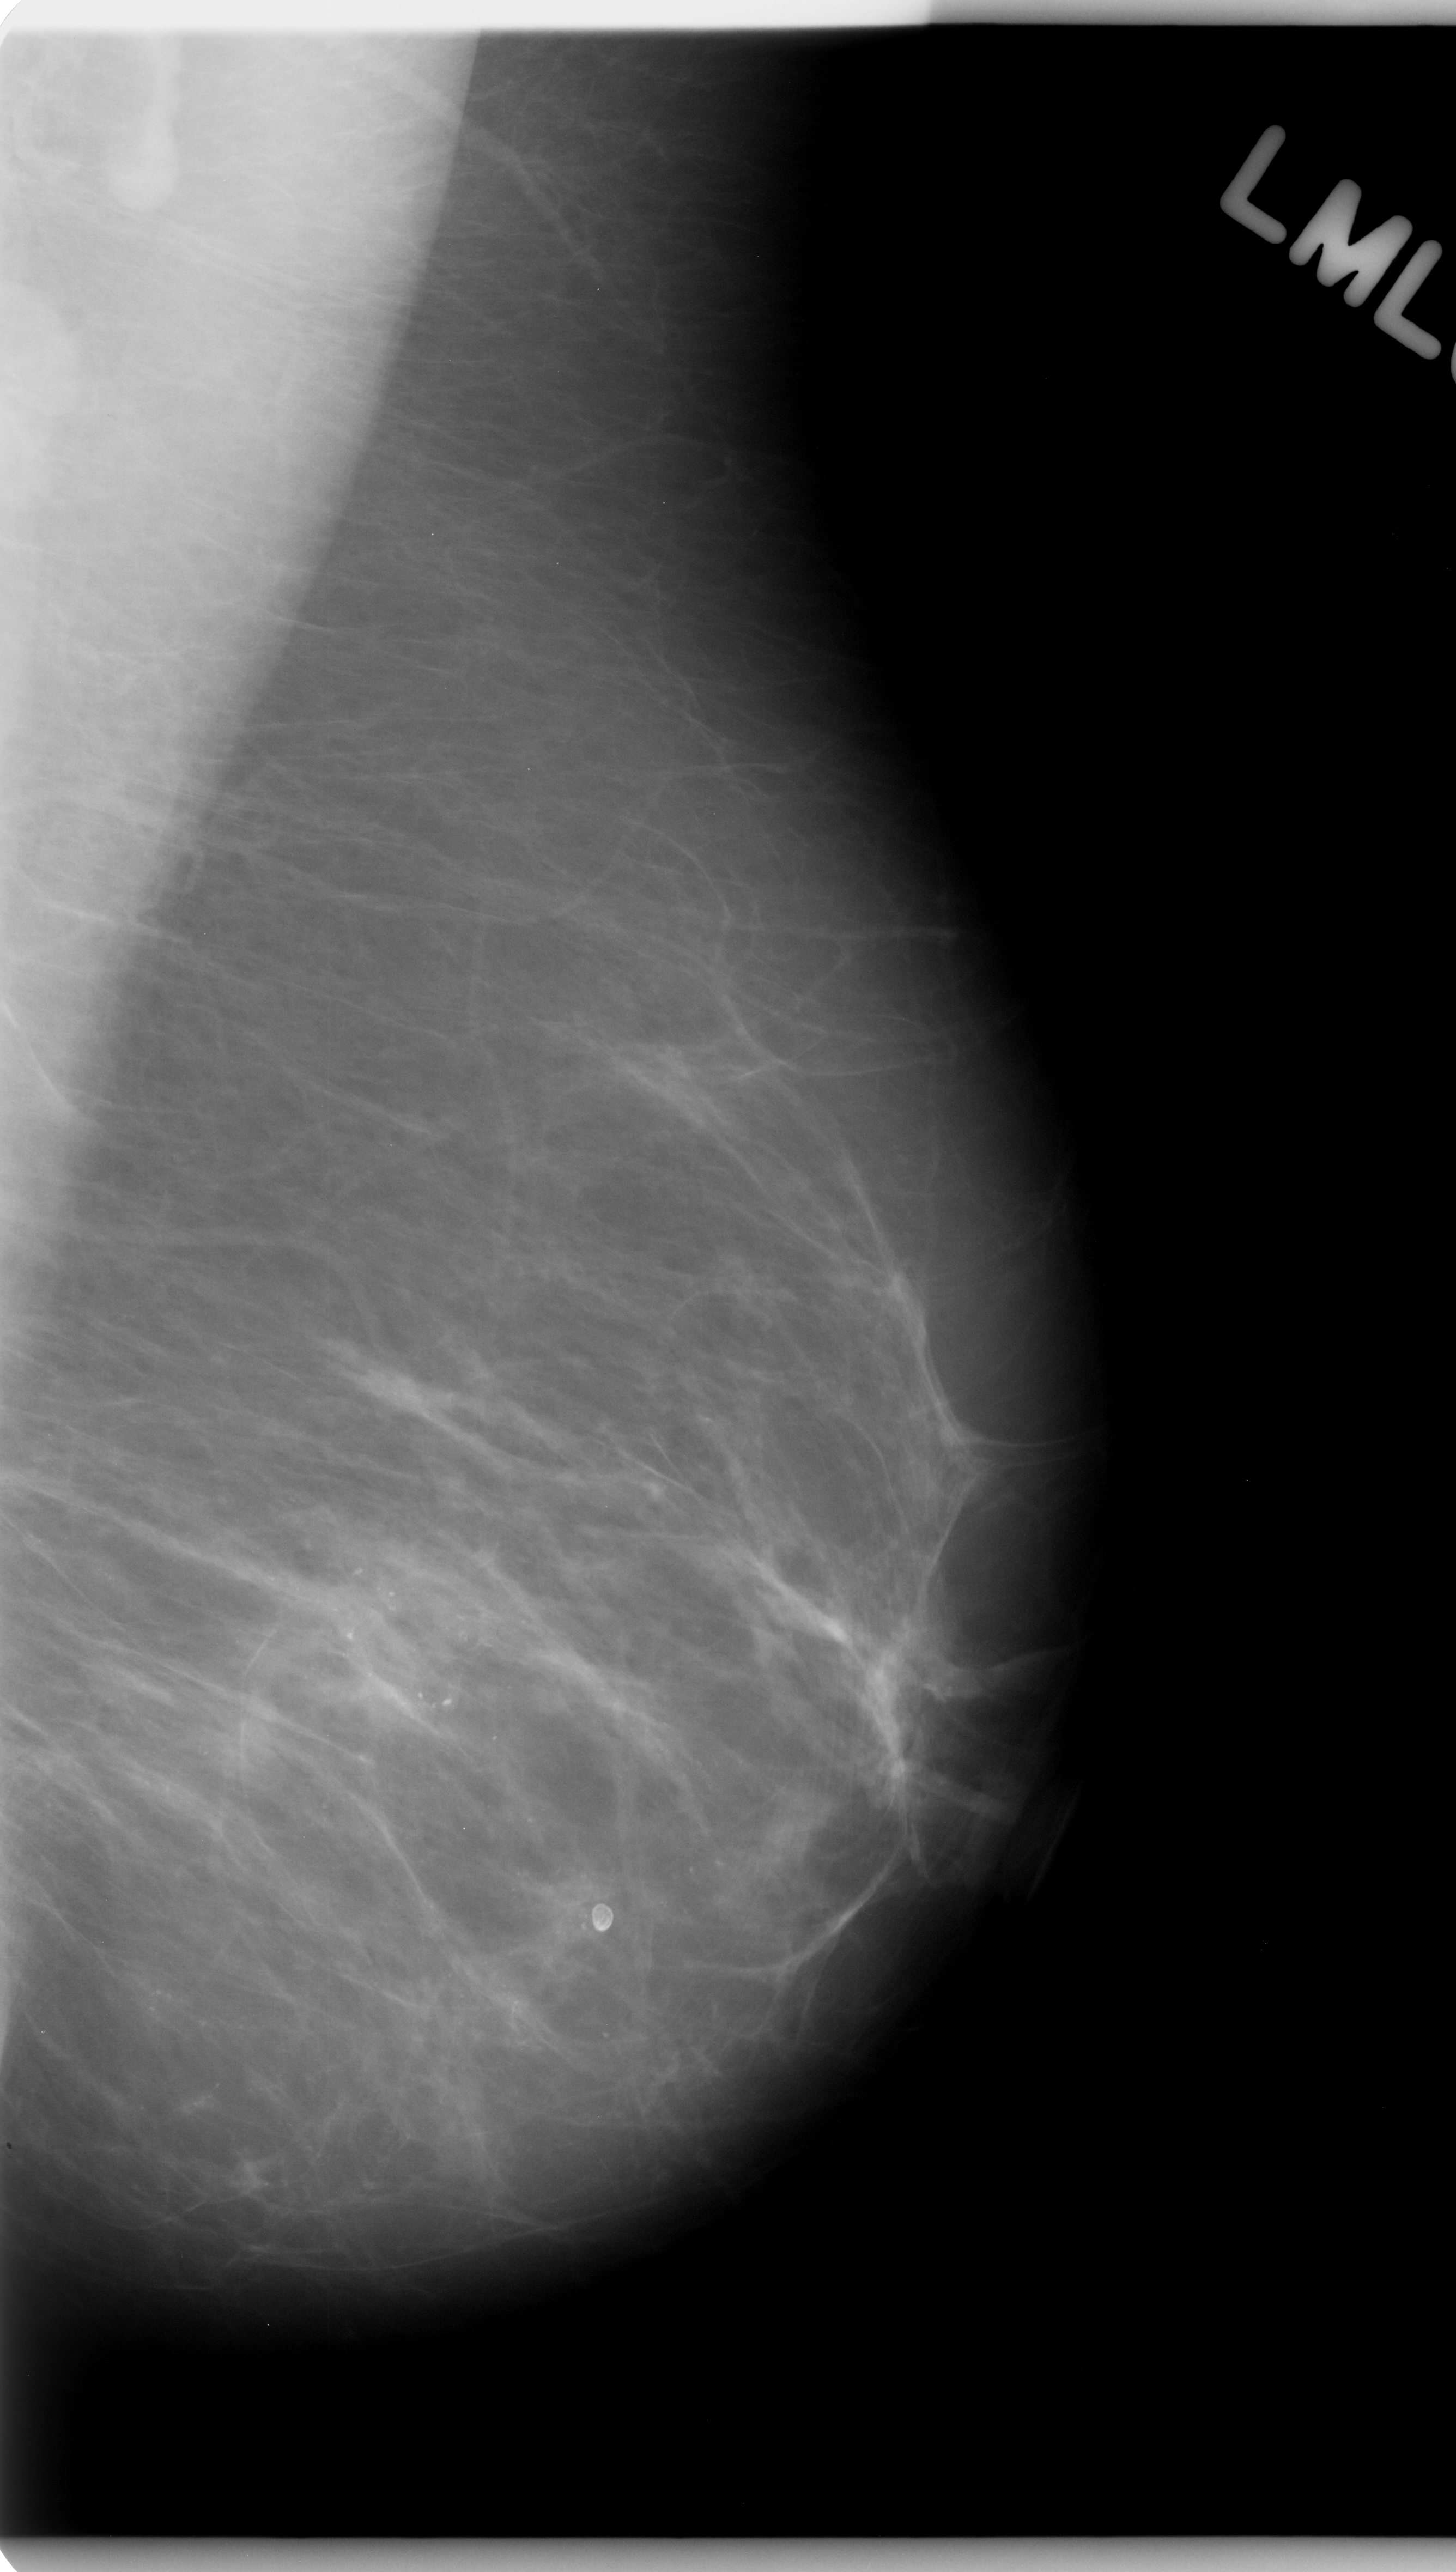
Digitized screen-film mammogram, left breast, MLO view.
Marked findings (only marked abnormalities are described; nothing is implied about the rest of the image): calcifications, morphology amorphous, distribution regional; BI-RADS assessment category 5; pathology result (as recorded, not read from the image): malignant.